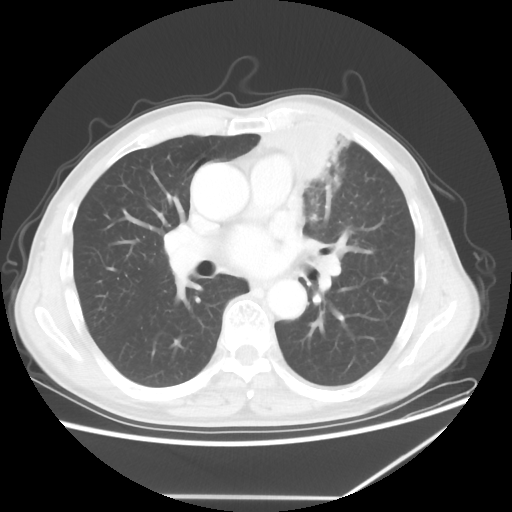
Chest CT, one axial slice; slice 34 of 64 in the series (ordered by position); reconstruction kernel STANDARD; lung window (W 1500 / L -600 HU); 512 × 512 image matrix, field of view 383 × 383 mm. Patient: male, 64 years. Case-level facts recorded for this patient, not image findings: clinical TNM (as recorded): T1c N1 M1; histopathological grade: G2.
Structures marked on this image (bounding box drawn by a radiologist):
- lung tumour (recorded histology: squamous cell carcinoma): bounding box [x1, y1, x2, y2] px = [256, 118, 395, 259]